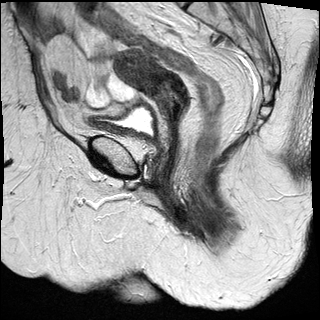
Pelvic MRI for cervical cancer, one sagittal slice; position 13 of 27 along the scan axis; T2-weighted; 1.5 T; TE 89 ms, TR 2740 ms; 4 mm slice thickness; 320 × 320 image matrix, field of view 260 × 260 mm. Female patient, age 67 years.
Annotated regions visible in this slice (expert manual segmentation):
- uterus and cervix: bounding box [x1, y1, x2, y2] px = [113, 48, 189, 123]